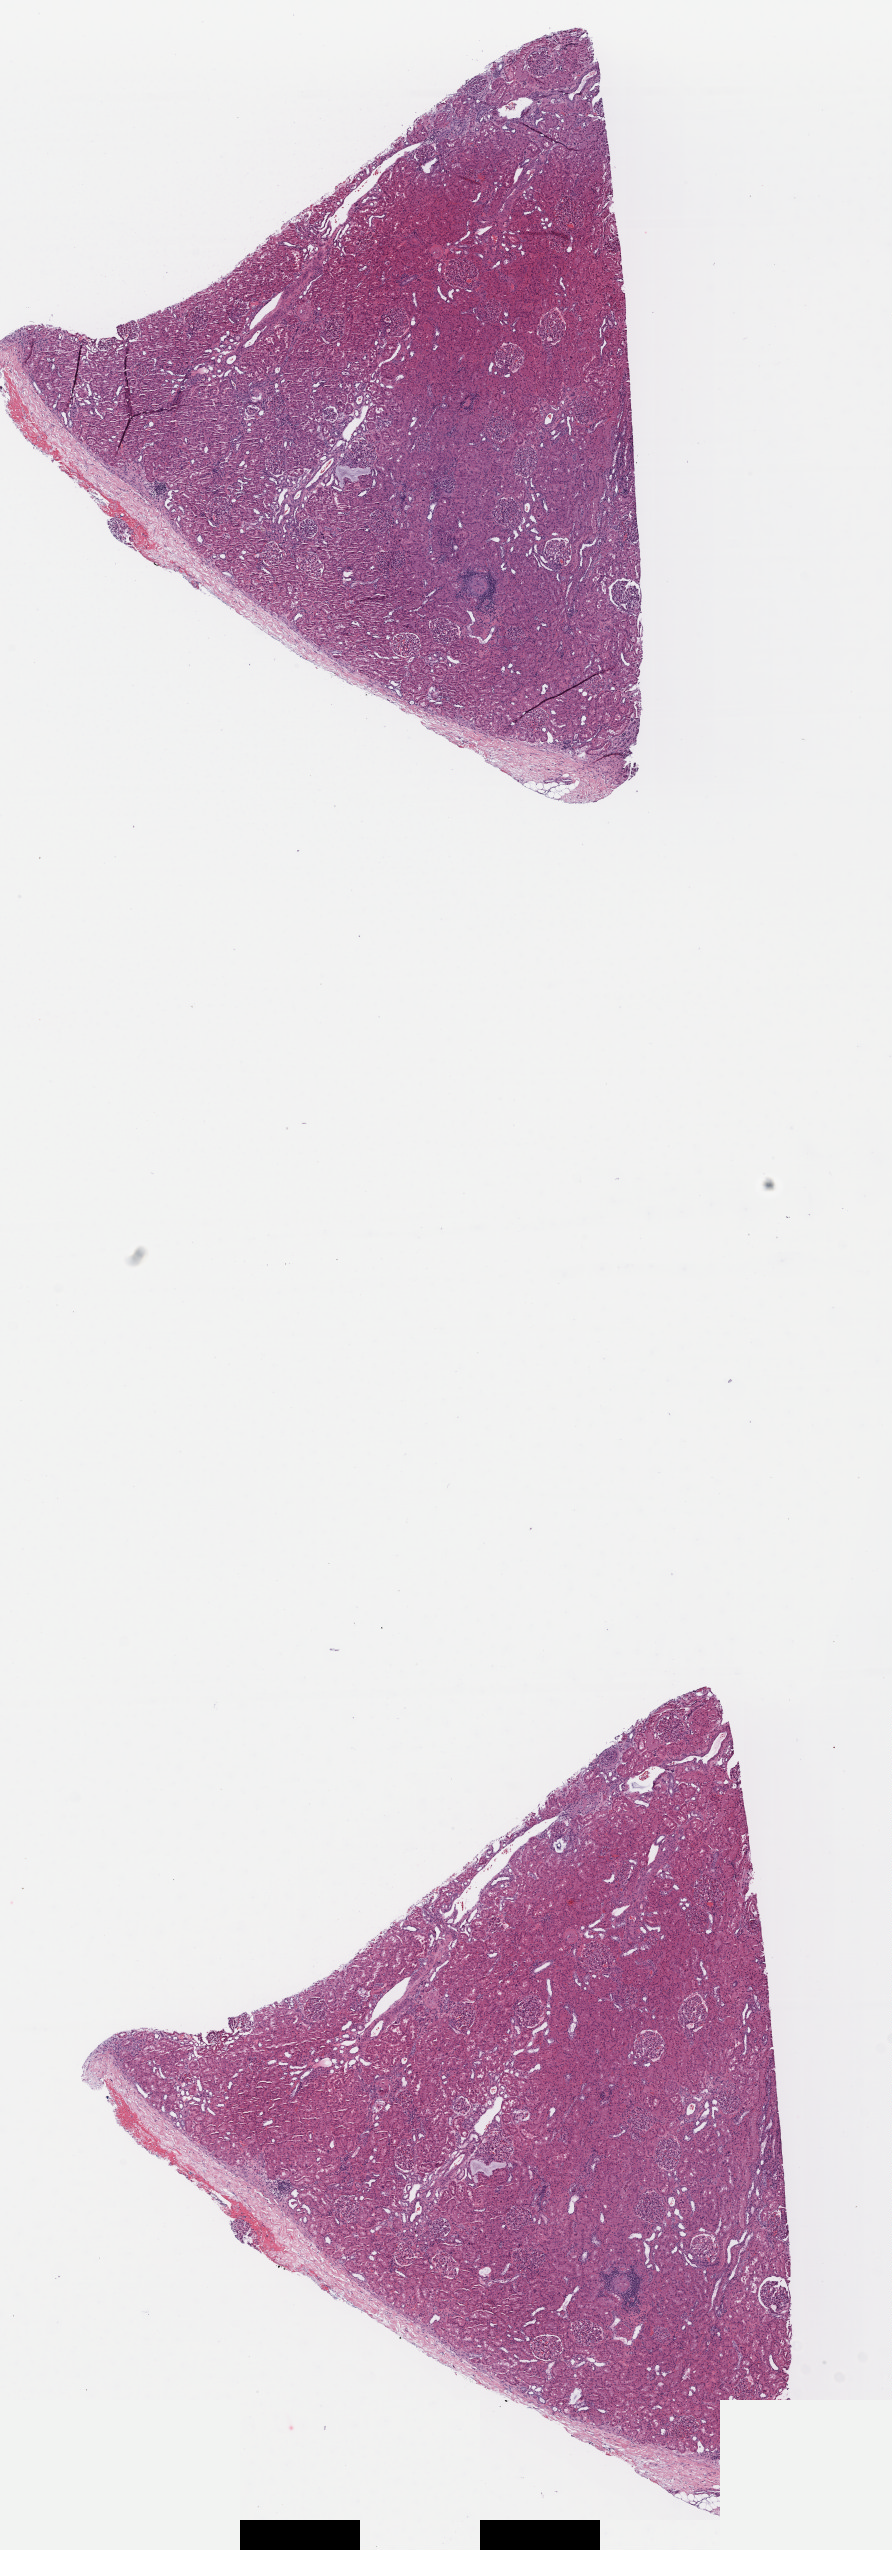
H&E whole-slide image, low-resolution overview of the scanned area, about 7.0 x 20.1 mm, formalin-fixed paraffin-embedded (FFPE) diagnostic section, kidney, primary tumour sample. Male, age 43 years at initial diagnosis.
* AJCC pathologic stage: I
* histologic diagnosis: Papillary adenocarcinoma, NOS